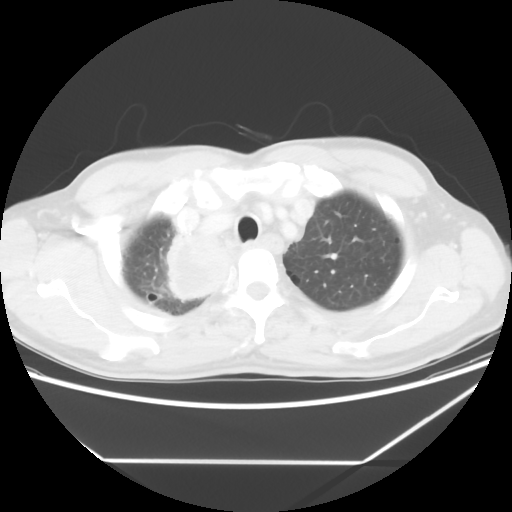
Chest CT, one axial slice. Slice 51 of 60 in the series (ordered by position). 120 kVp. Lung window (W 1500 / L -600 HU). 5 mm slice thickness. 512 × 512 image matrix. Male patient, age 58 years. From the clinical record (not read from this slice): clinical TNM (as recorded): T2 N2 M0.
Structures marked on this image (rectangle marked by the reading radiologist):
- lung tumour (recorded histology: squamous cell carcinoma): bounding box [x1, y1, x2, y2] px = [159, 224, 233, 303]